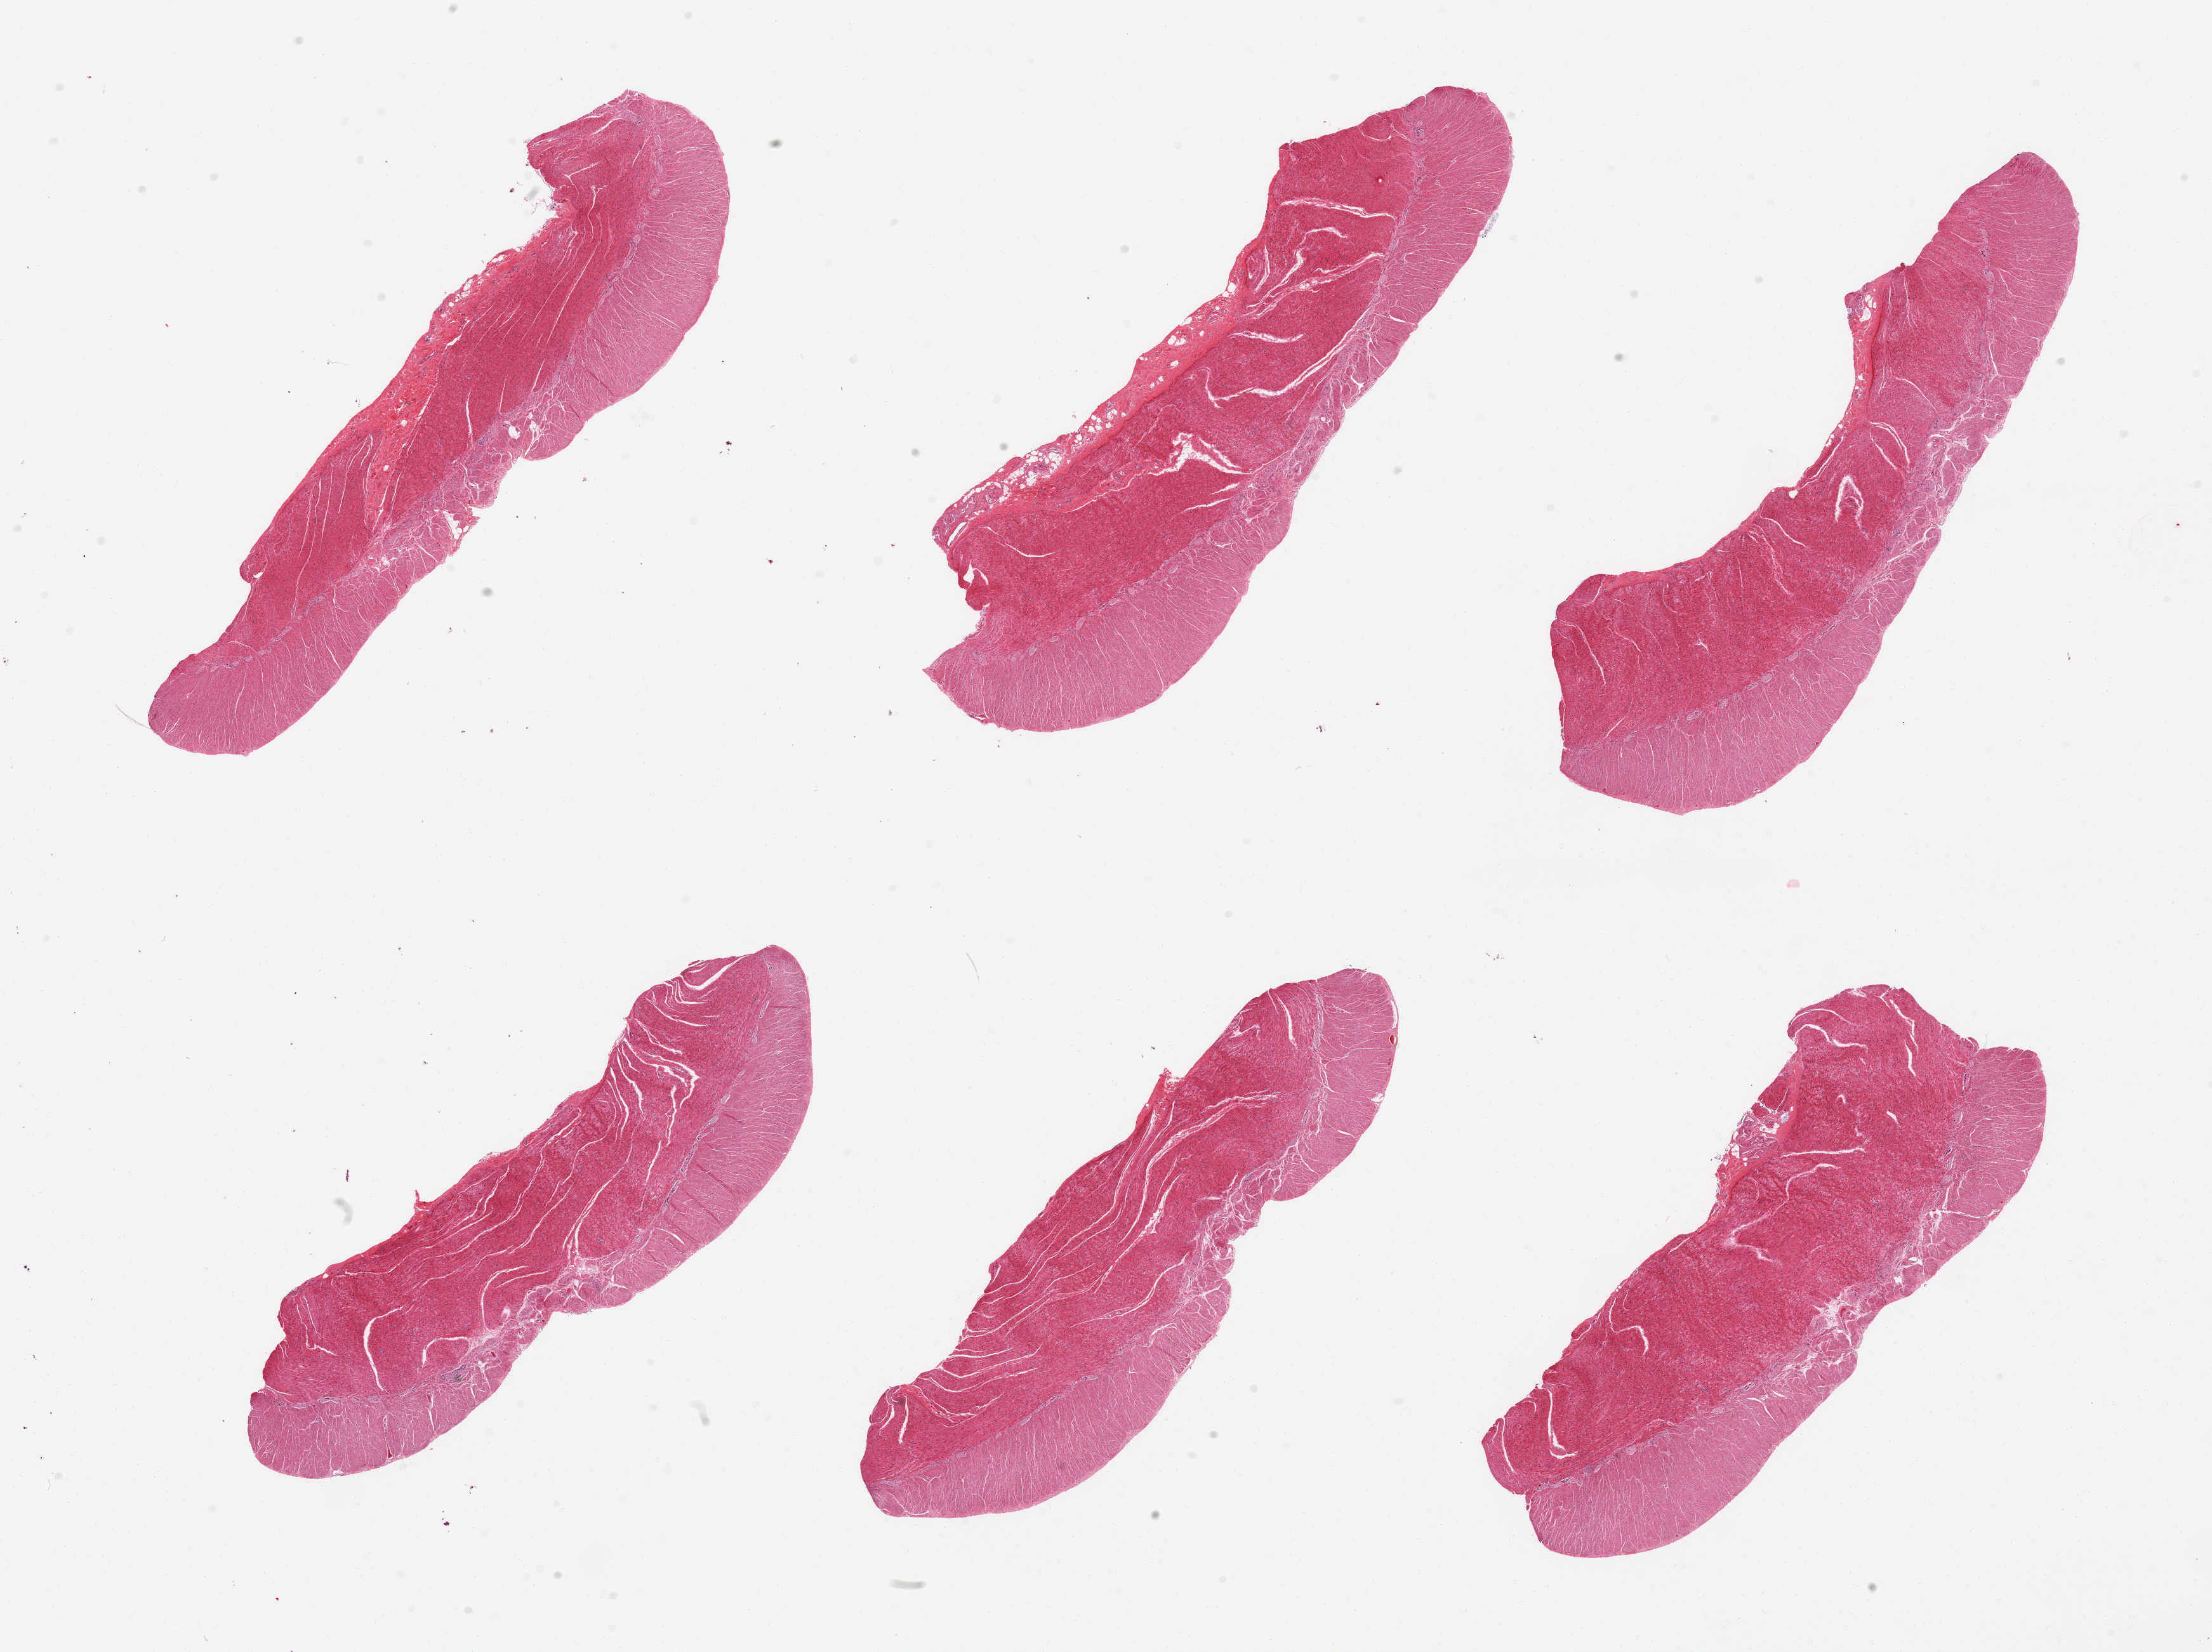
Digitized H&E-stained section, whole scanned area (about 27.6 x 20.6 mm, from a 20x scan) shown as a low-resolution overview; PAXgene-fixed paraffin-embedded (PFPE) section; sampled site (target tissue): sigmoid colon; tissue donor sample.
• reviewer comment on this tissue sample: 6 pieces; well dissected muscularis